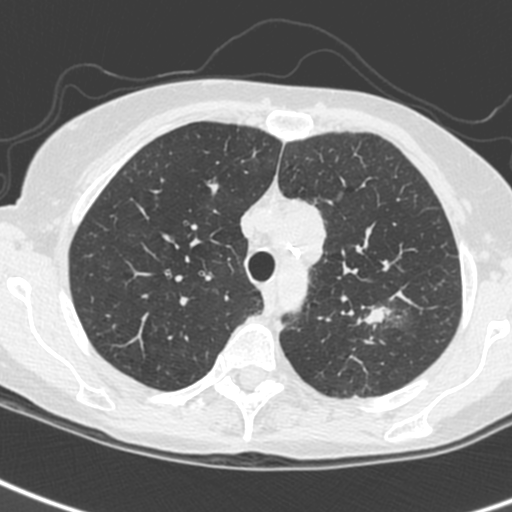
Low-dose screening chest CT, one axial slice. Slice 192 of 242 in the series (ordered by position). Lung window (W 1500 / L -600 HU). 1.3 mm slice thickness. 512 × 512 image matrix, field of view 284 × 284 mm.
Structures marked on this image (manually delineated by an expert):
- lesion 1 (tumor, upper lobe of left lung): box from (x=364, y=307) to (x=386, y=324) px
- lesion 3 (tumor, upper lobe of left lung): (x=294, y=200)–(x=326, y=267)